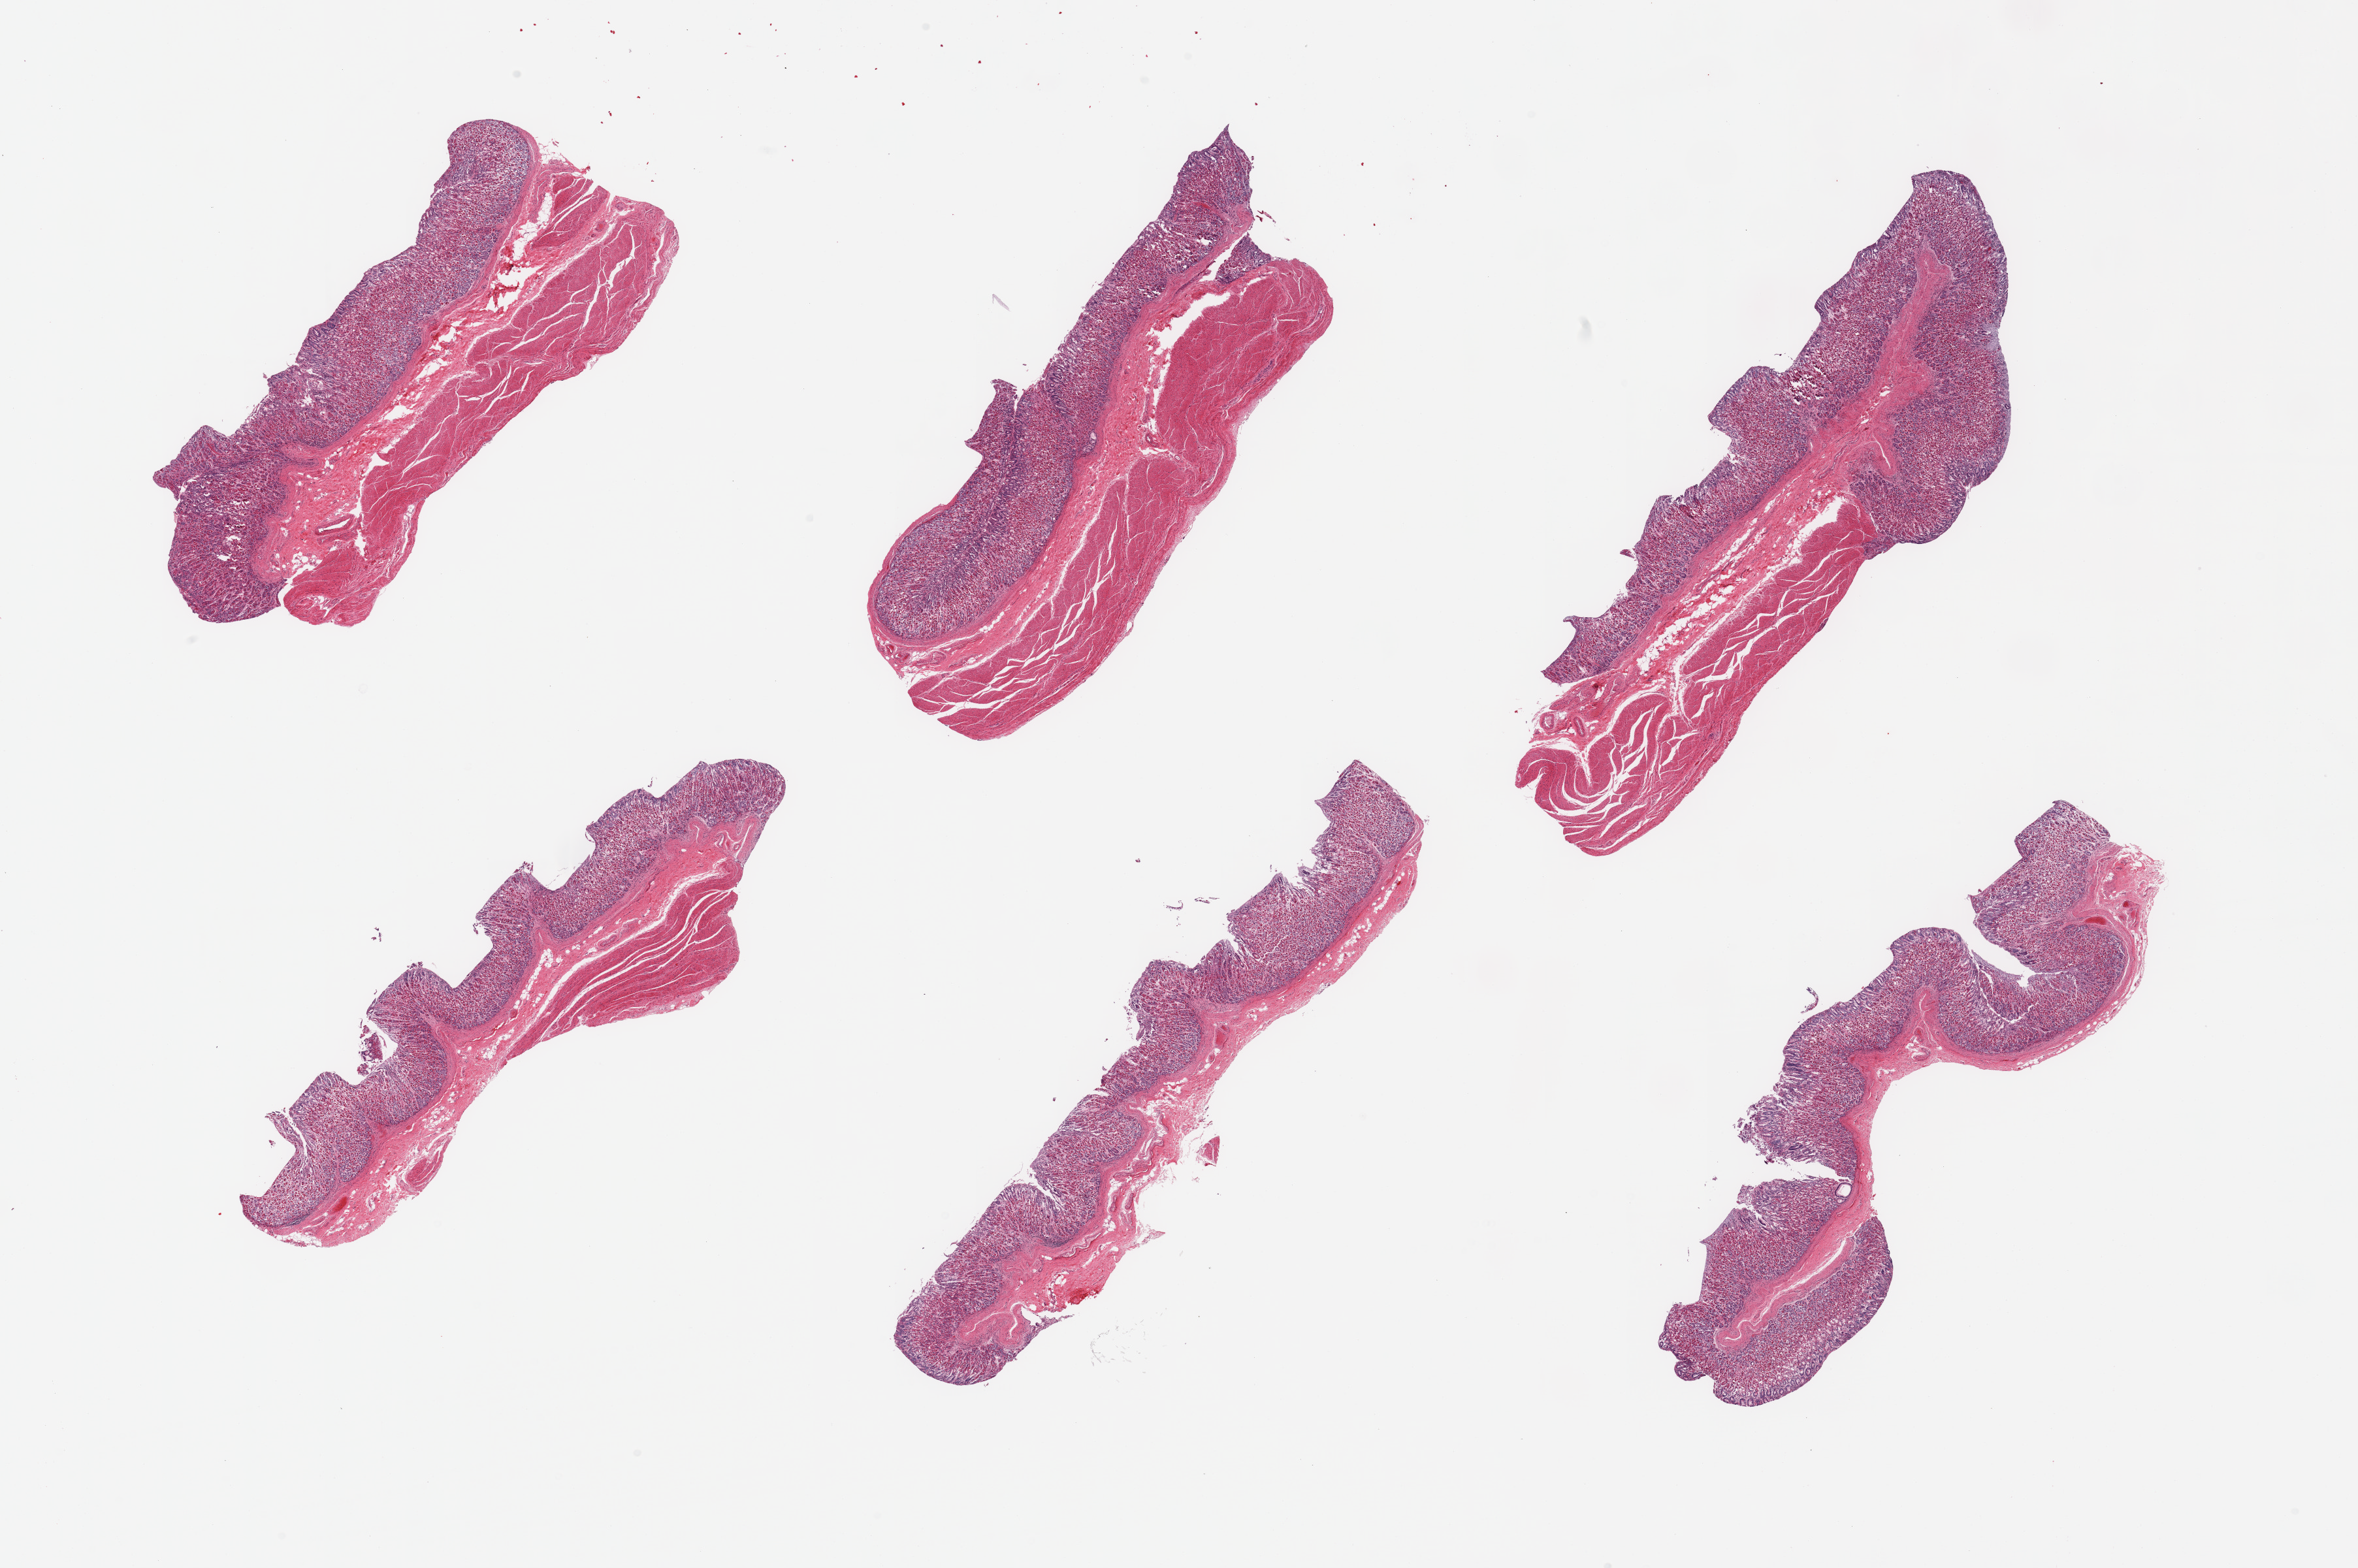
Digitized hematoxylin and eosin (H&E)-stained section — low-resolution overview of the scanned area, about 28.5 x 19.0 mm (acquisition: 20x scan). PAXgene-fixed paraffin-embedded (PFPE) section. Target tissue: stomach. Tissue donor sample. Donor sex: male.
Reviewer comment on this tissue sample: 6 pieces, mucosa up to ~1mm, 40-90% thickness, moderately advanced autolysis.